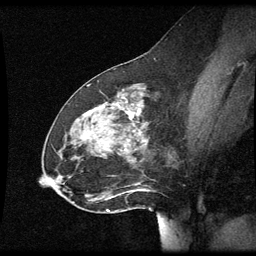
Breast MRI (dynamic contrast-enhanced), one sagittal slice; slice 28 of 60 in the series (ordered by position); dynamic contrast-enhanced series, image 2 of 3 at this slice position (ordered by acquisition); 1.5 T; TE 4.2 ms, TR 8.9 ms; 2 mm slice thickness; 256 × 256 image matrix, field of view 200 × 200 mm. Female patient, age 49 years. Case-level facts recorded for this patient, not image findings: setting: breast cancer imaged before/during neoadjuvant chemotherapy; receptor status: HR-positive, HER2-negative.
Outlined on this slice (semi-automatic segmentation, software-assisted and operator-edited):
- analysis volume of interest (the breast-tissue region the enhancement analysis was run in; not a lesion): bounding box <46,92,155,205> (left, top, right, bottom; pixels)
- tumour enhancement mask (voxels above the 70 % enhancement threshold inside the analysis volume of interest): <117,104,141,119>